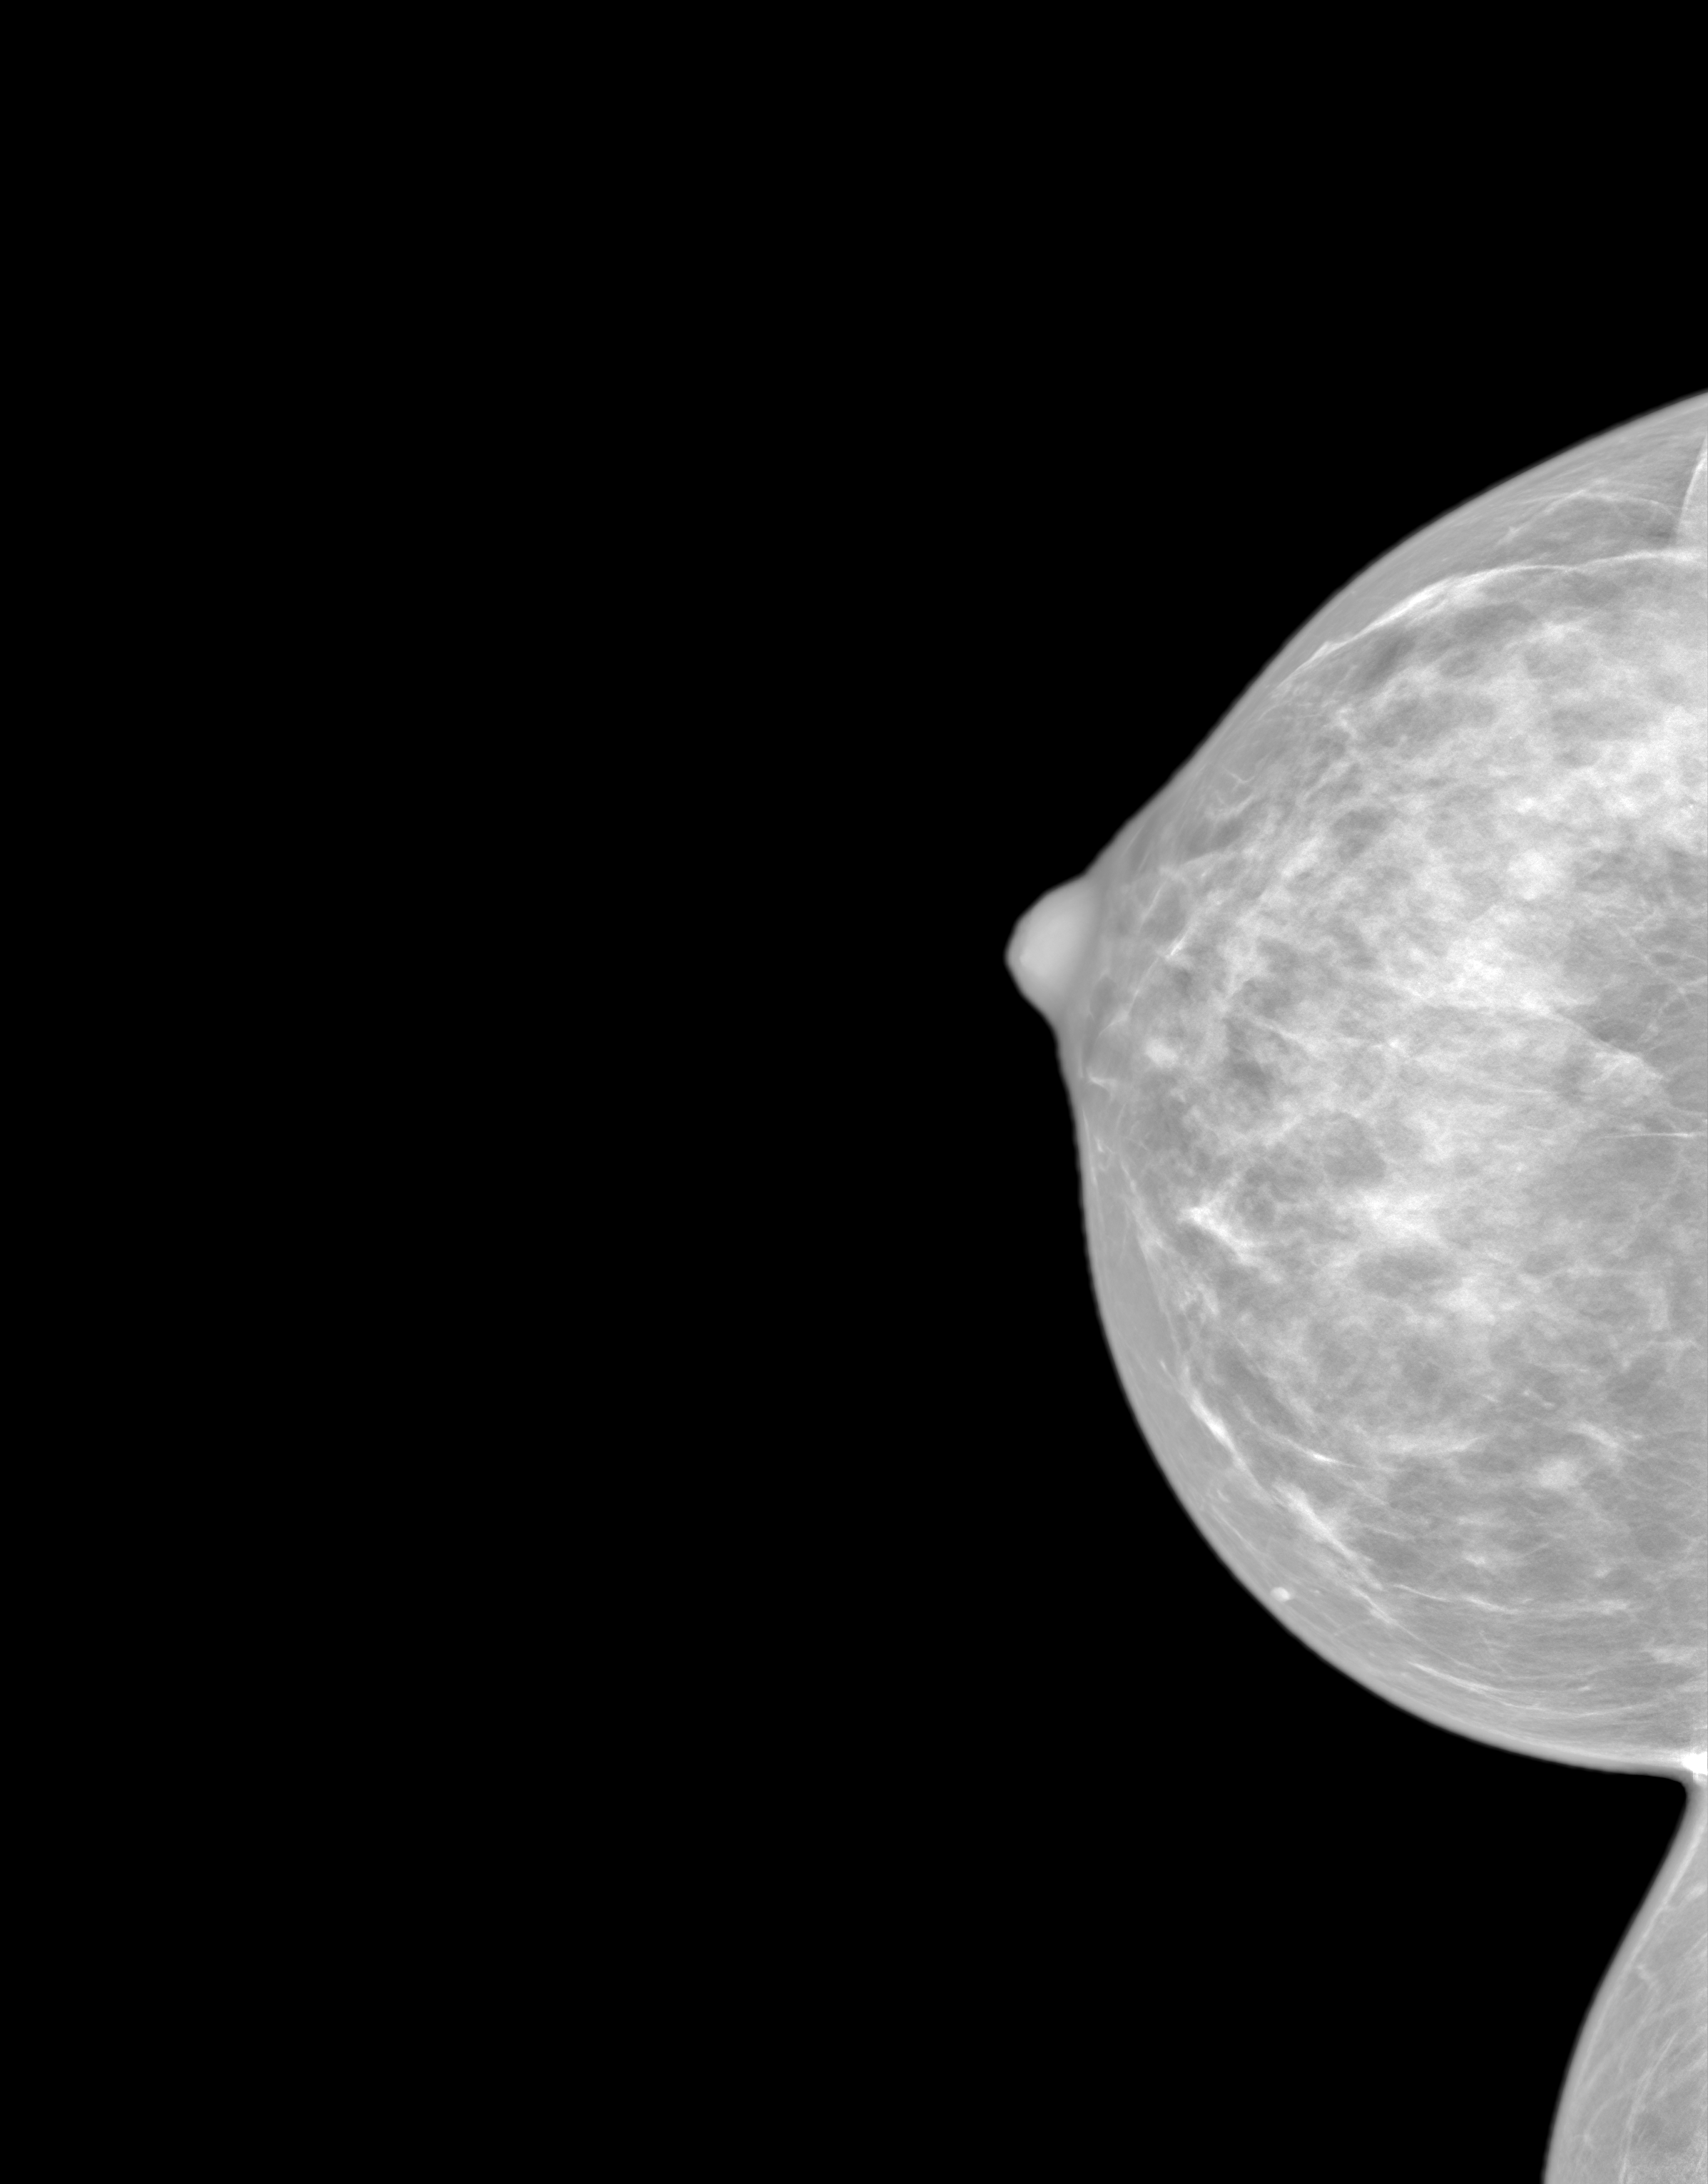
Synthesized 2-D mammogram reconstructed from digital breast tomosynthesis, right breast, cranio-caudal projection, screening examination. Patient aged 42 years (female).
Breast density at the screening exam (both breasts): extremely dense (BI-RADS density category d). Final BI-RADS assessment for this screening round (tomosynthesis exam, both breasts): category 1. Recall: no recall after this screen.